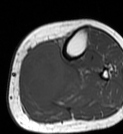
MRI of an extremity soft-tissue mass, one axial slice. Slice 25 of 68 in the series (ordered by position). MR volume resampled by the dataset authors to the PET/CT grid (not the native acquisition matrix). 3.27 mm slice thickness. 123 × 134 image matrix, field of view 120 × 131 mm. Female patient. From the clinical record (not read from this slice): histological type: extraskeletal high grade osteogenic sarcoma; grade: high; site of the primary tumour: left calf.
Structures marked on this image (expert contour drawn on MRI and transferred to this co-registered scan by the dataset authors):
- gross tumour volume (mass): bounding box [x1, y1, x2, y2] px = [19, 43, 66, 102]